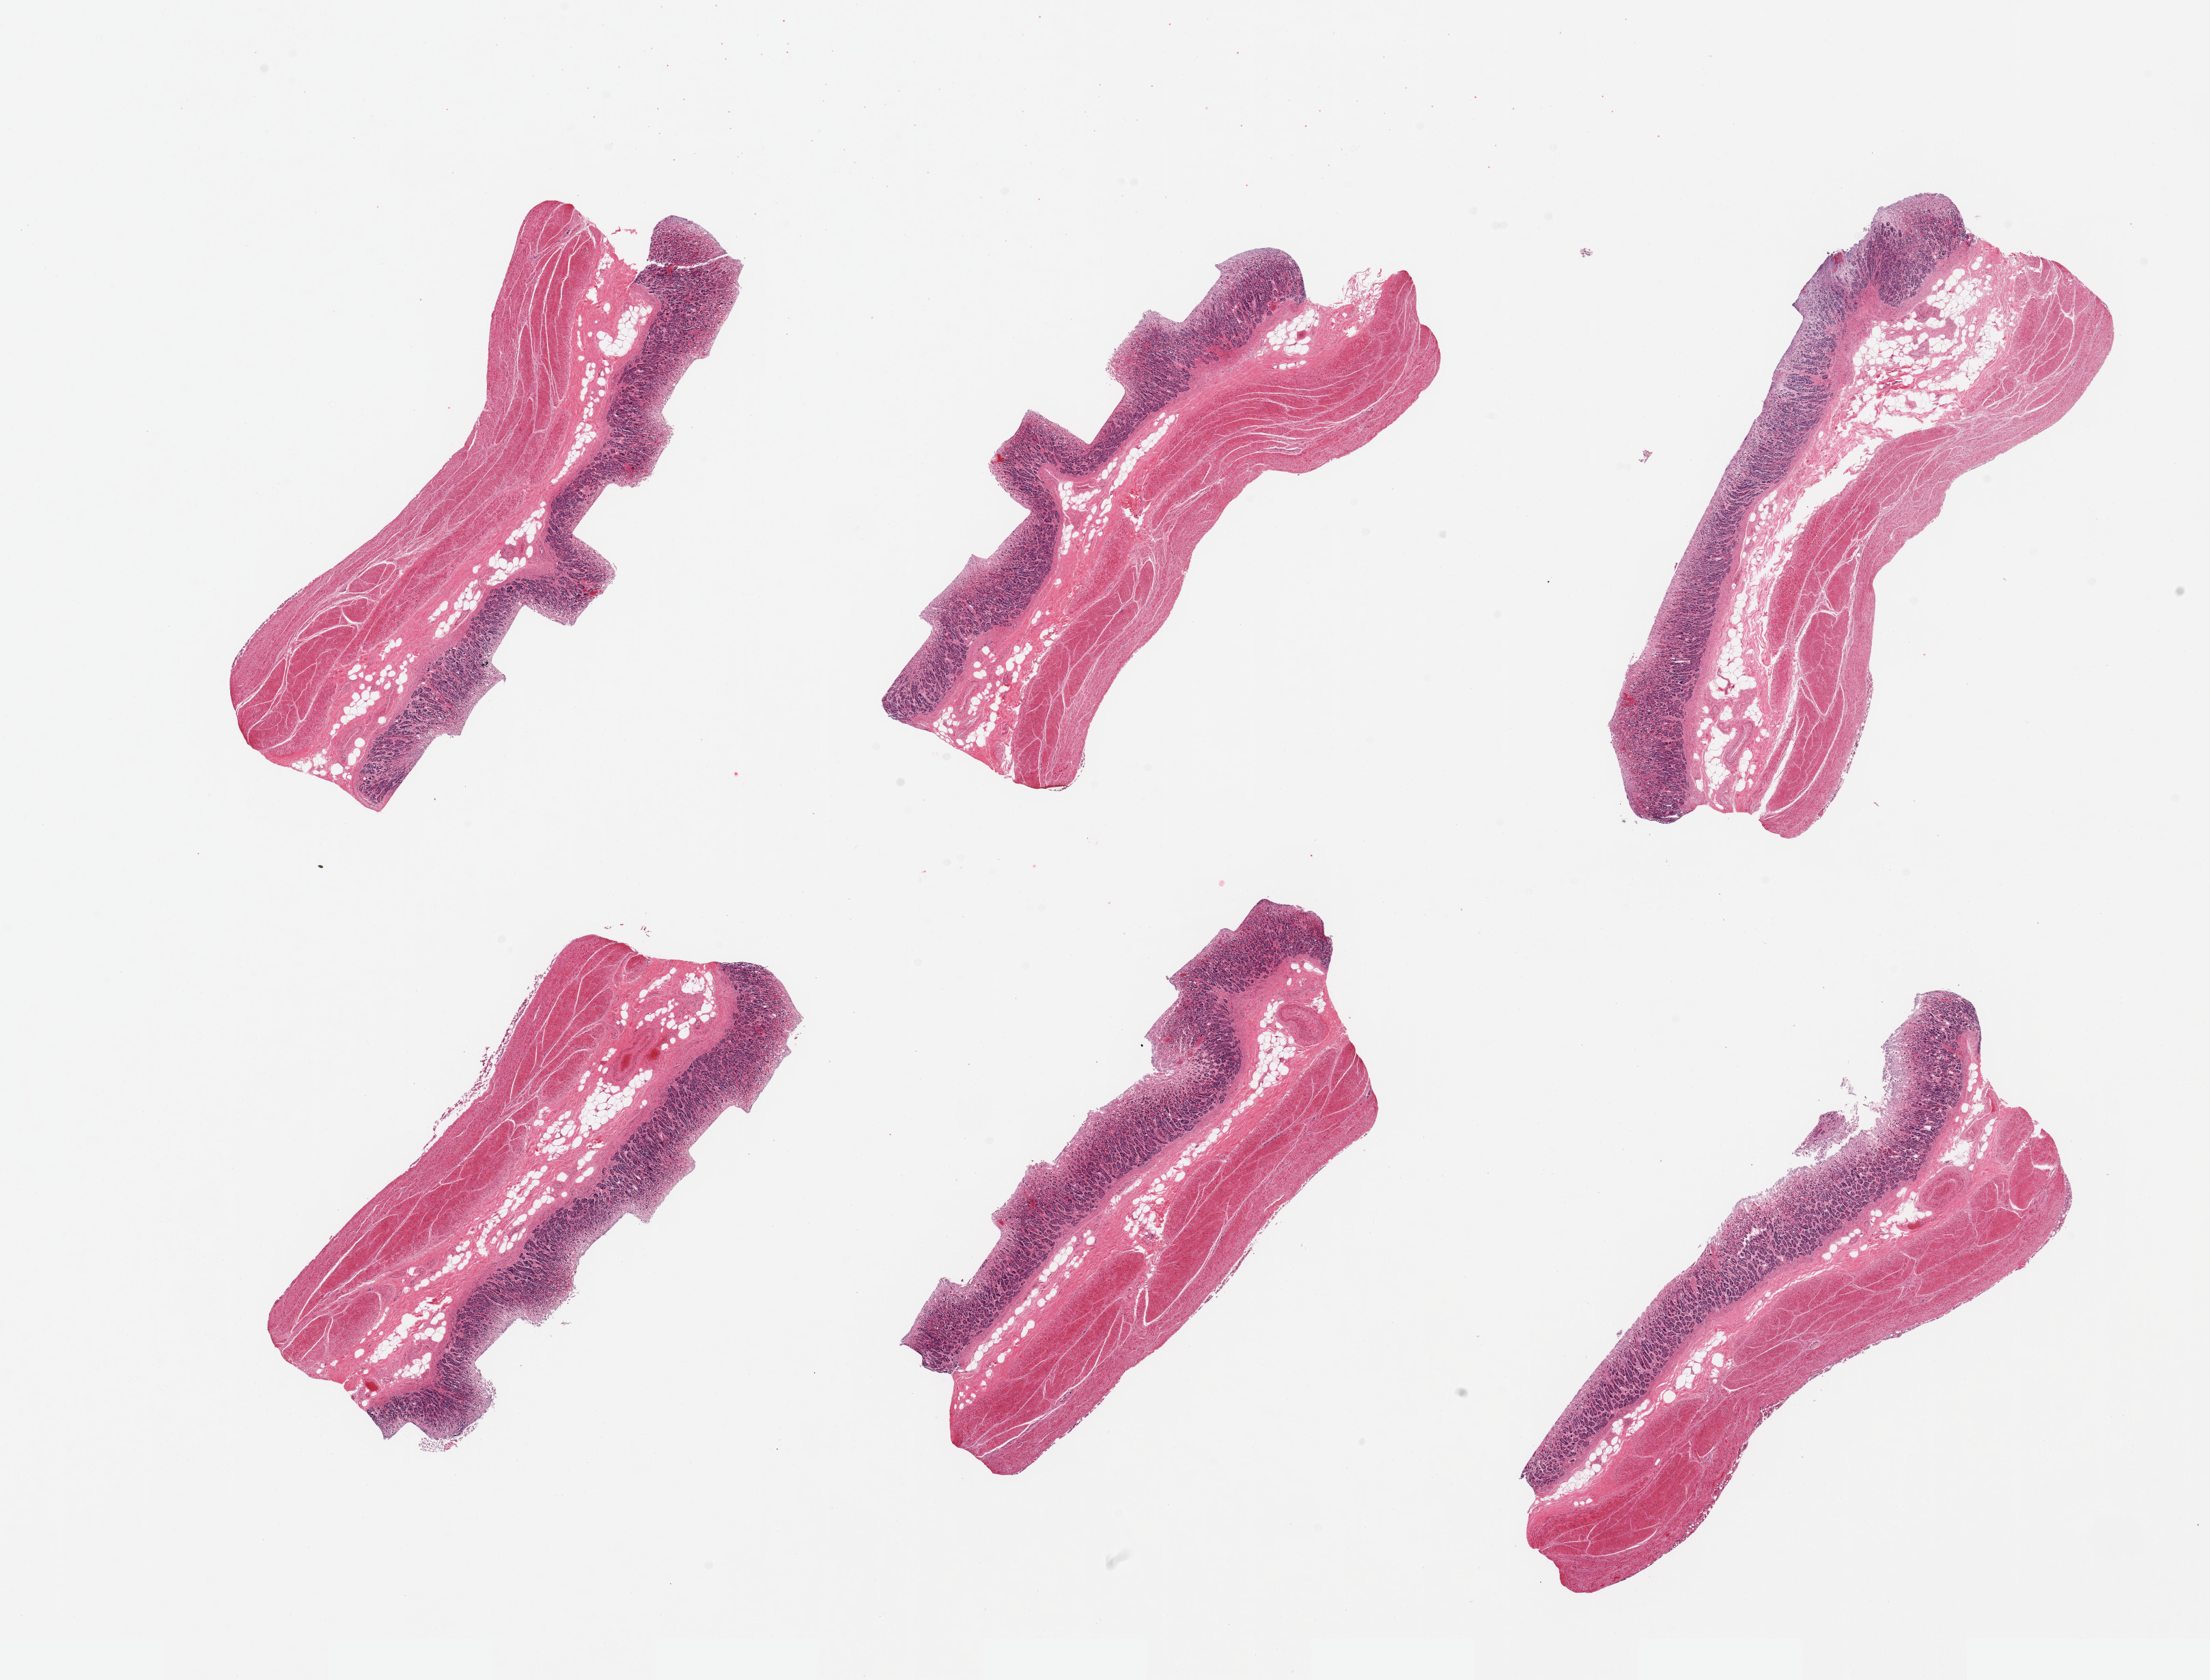
H&E whole-slide image, low-resolution overview of the scanned area, about 25.6 x 19.5 mm; PAXgene-fixed, paraffin-embedded tissue; target tissue: stomach; donor tissue sample. Donor: male.
Reviewer comment on this tissue sample: 6 pieces, target mucosa is ~0.7mm, ~30-35% thickness.